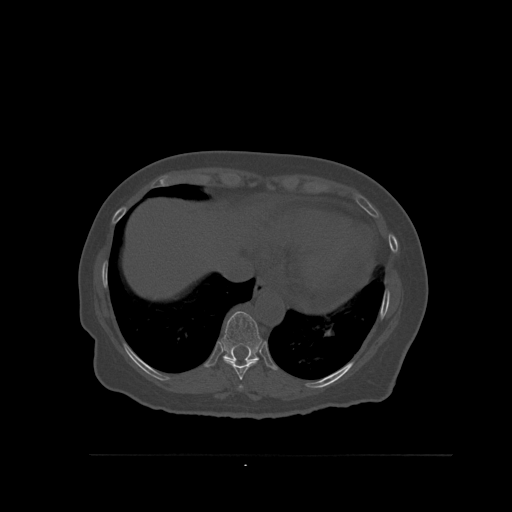
CT including the spine, one axial slice; position 327 of 527 along the scan axis; bone window (W 1800 / L 400 HU); 512 × 512 image matrix, field of view 470 × 470 mm. Female patient, age 73 years. From the clinical record (not read from this slice): primary cancer: breast.
Structures marked on this image (semi-automatically segmented with operator editing):
- T10 vertebra: bounding box [x1, y1, x2, y2] px = [221, 311, 262, 361]
- T8 vertebra: [238, 385, 243, 390]
- T9 vertebra: [223, 358, 259, 380]